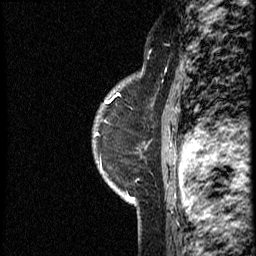
Breast MRI (dynamic contrast-enhanced), one sagittal slice; slice 30 of 40 in the series (ordered by position); dynamic contrast-enhanced study with each time point stored as its own series, time point 2 of 4 at this slice position (early post-contrast, ordered by acquisition time); 1.5 T; TE 4.2 ms, TR 18.8 ms; 3 mm slice thickness; 256 × 256 image matrix, field of view 200 × 200 mm. Female patient. Case-level facts recorded for this patient, not image findings: setting: breast cancer imaged before/during neoadjuvant chemotherapy; receptor status: HER2-positive.
Structures marked on this image (semi-automatic segmentation, software-assisted and operator-edited):
- analysis volume of interest (the breast-tissue region the enhancement analysis was run in; not a lesion): box from (x=93, y=79) to (x=165, y=153) px
- tumour enhancement mask (voxels above the 100 % enhancement threshold inside the analysis volume of interest): (x=98, y=94)–(x=121, y=134)